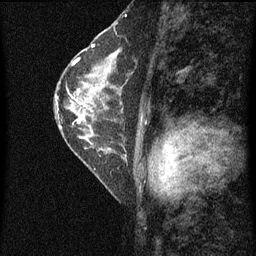
Breast MRI (dynamic contrast-enhanced), one sagittal slice; slice 39 of 60 in the series (ordered by position); dynamic contrast-enhanced series, image 2 of 4 at this slice position (ordered by acquisition); 1.5 T; TE 4.2 ms, TR 8 ms; 2 mm slice thickness; 256 × 256 image matrix. Female patient, age 56 years.
Outlined on this slice (semi-automatically segmented with operator editing):
- analysis volume of interest (the breast-tissue region the enhancement analysis was run in; not a lesion): bounding box (x1, y1, x2, y2) in pixels: (56, 52, 128, 115)
- tumour enhancement mask (voxels above the 70 % enhancement threshold inside the analysis volume of interest): (76, 56, 117, 109)